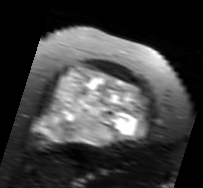
MRI of an extremity soft-tissue mass, one axial slice. Slice 54 of 91 in the series (ordered by position). T2-weighted fat-saturated. MR volume resampled by the dataset authors to the PET/CT grid (not the native acquisition matrix). 203 × 188 image matrix, field of view 198 × 184 mm. Female patient. Case-level facts recorded for this patient, not image findings: histological type: malignant solitary fibrous tumor; grade: intermediate; site of the primary tumour: right thigh.
Annotated regions visible in this slice (expert contour drawn on MRI and transferred to this co-registered scan by the dataset authors):
- gross tumour volume including surrounding oedema: bounding box (x1, y1, x2, y2) in pixels: (33, 65, 150, 148)
- gross tumour volume (mass): (33, 67, 146, 146)